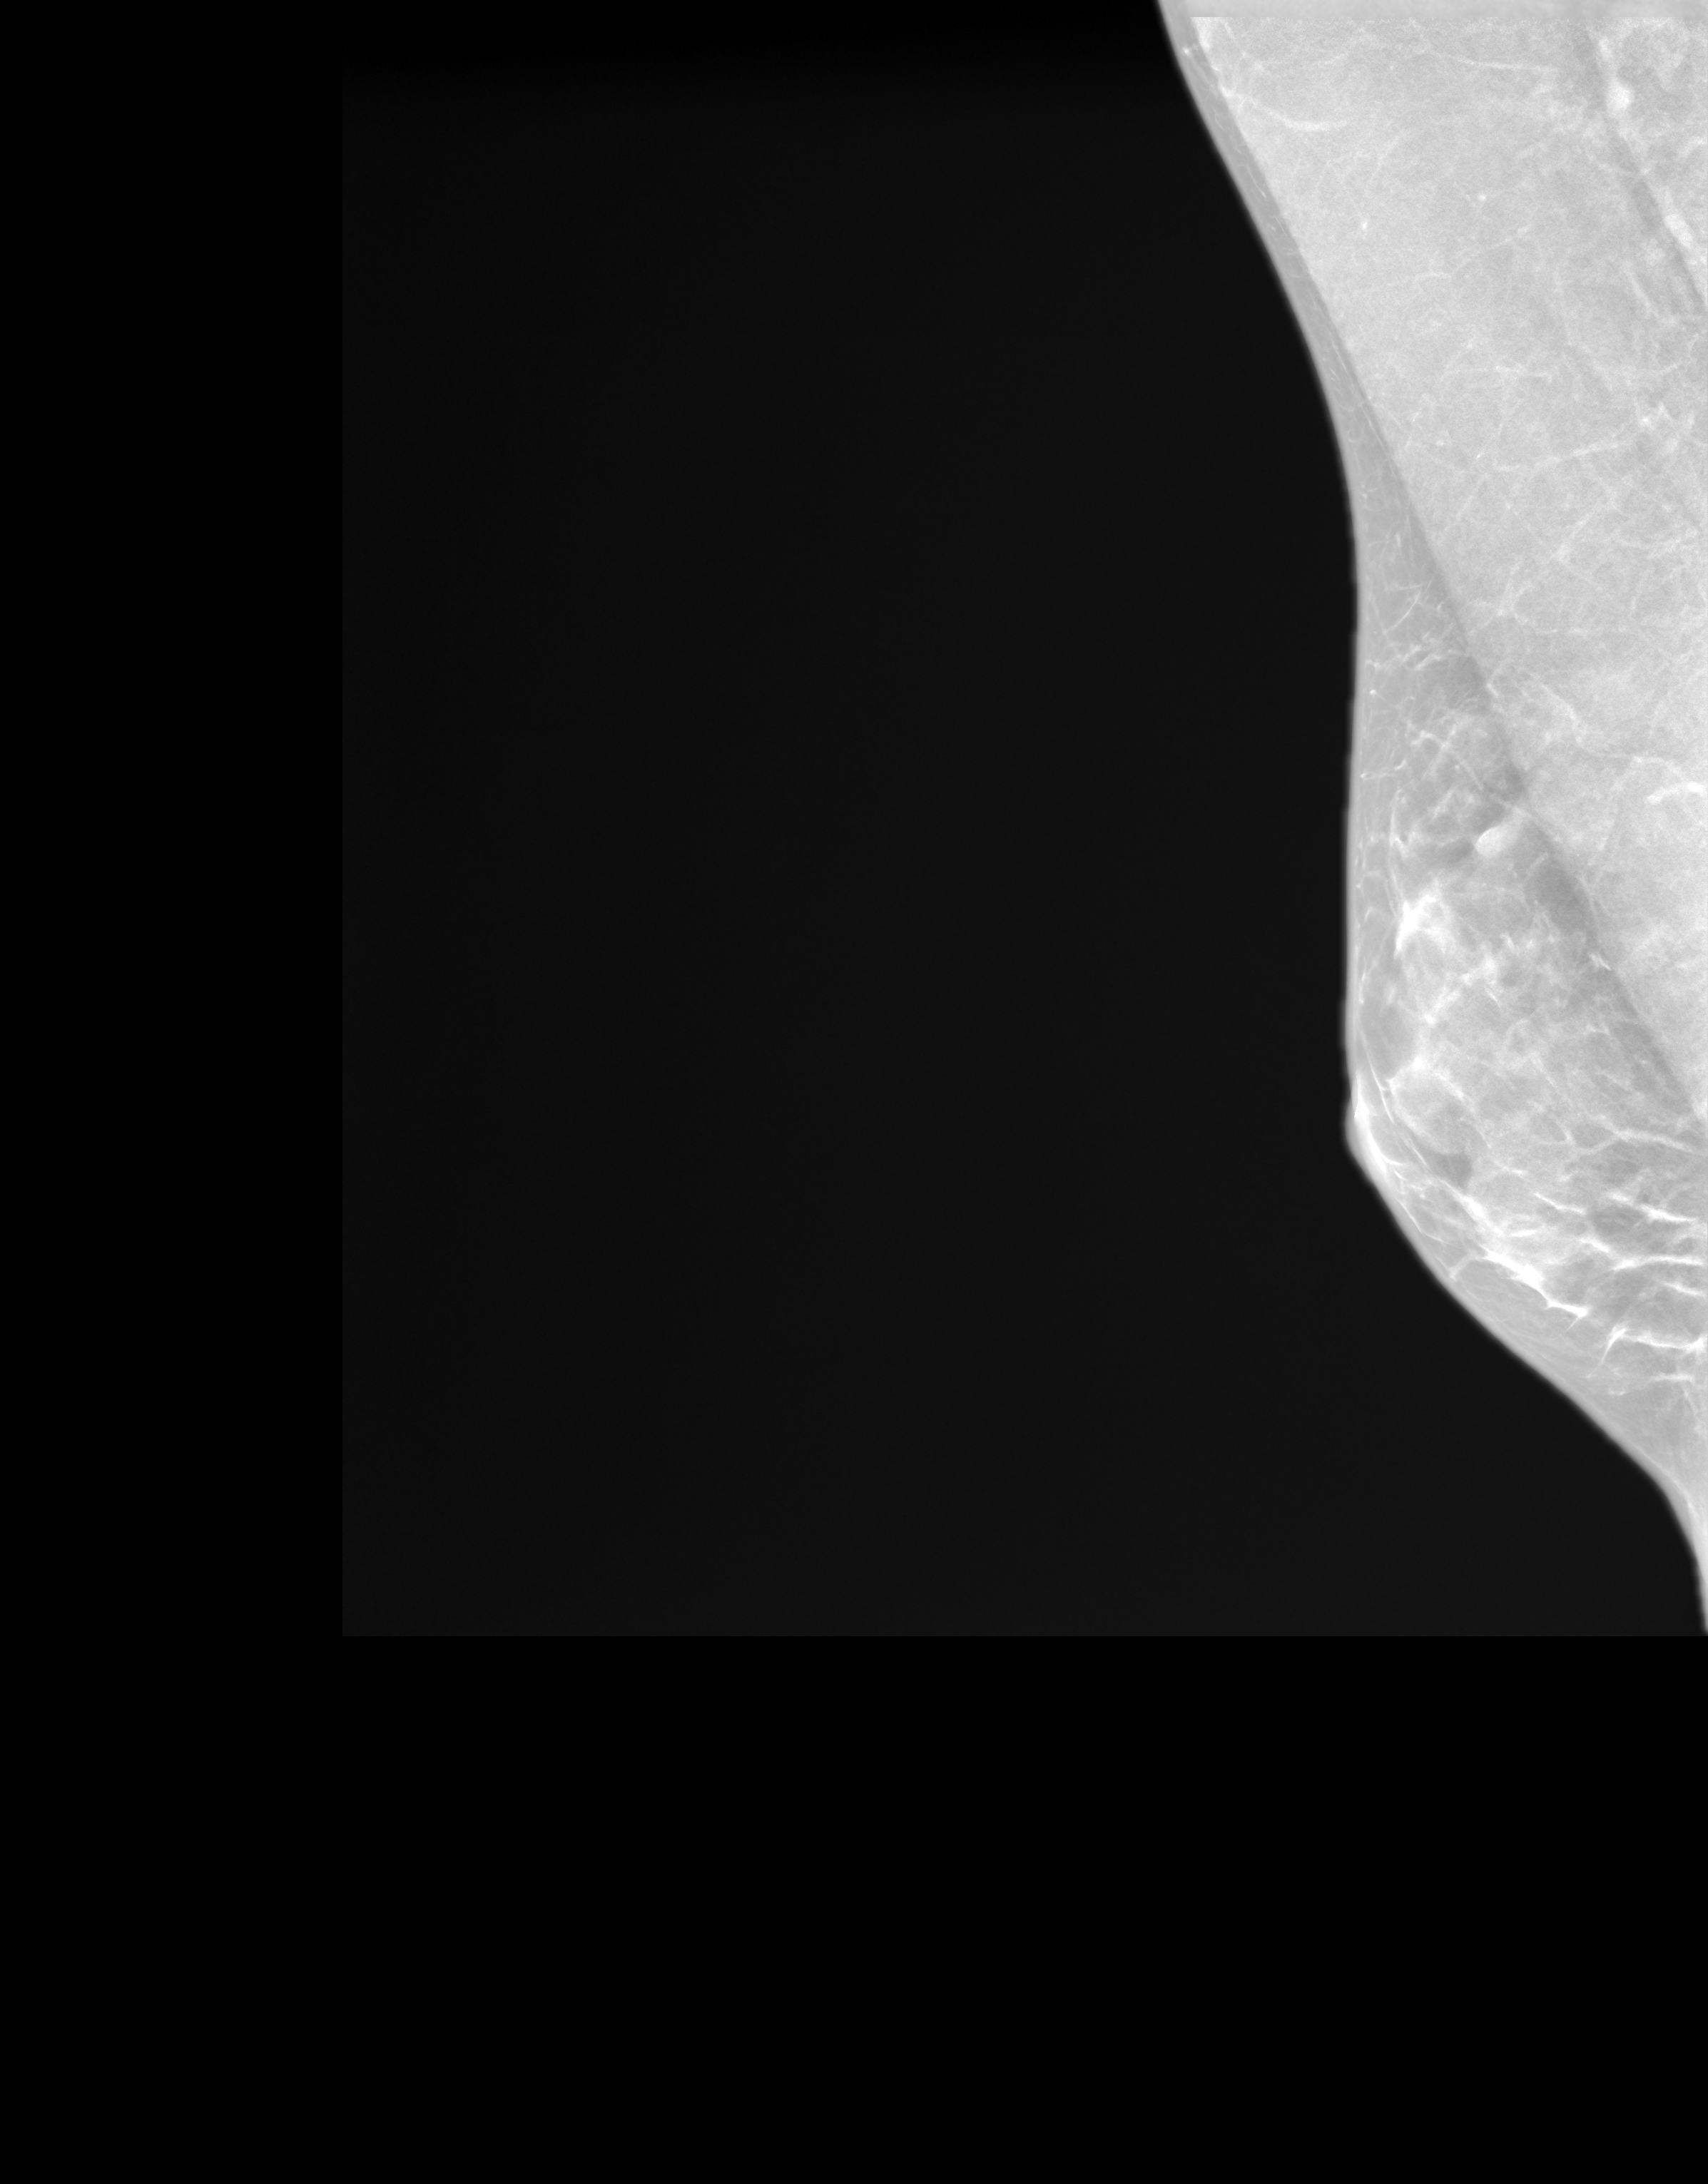
Screening examination, system: SenoIris_1SP1.1(421). Patient aged 55 years (female).
Image type: synthesized 2-D view from tomosynthesis. Breast: right. Projection: medio-lateral oblique projection.